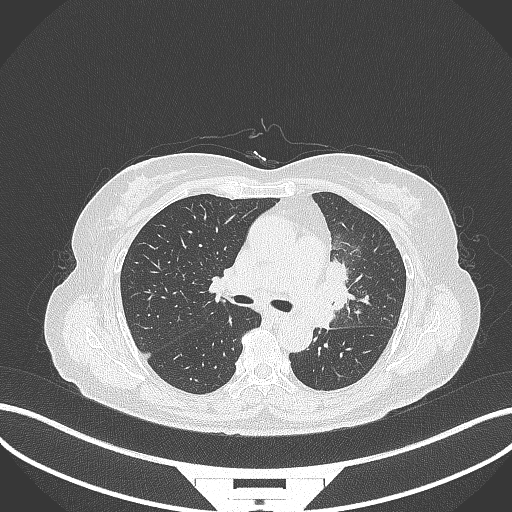
Chest CT, one axial slice; slice 204 of 382 in the series (ordered by position); 120 kVp; lung window (W 1500 / L -600 HU); 1 mm slice thickness; 512 × 512 image matrix, field of view 400 × 400 mm. Female patient, age 64 years. Case-level facts recorded for this patient, not image findings: clinical TNM (as recorded): T2a N2 M0.
Outlined on this slice (bounding box drawn by a radiologist):
- lung tumour (recorded histology: adenocarcinoma): bounding box <321,249,357,335> (left, top, right, bottom; pixels)